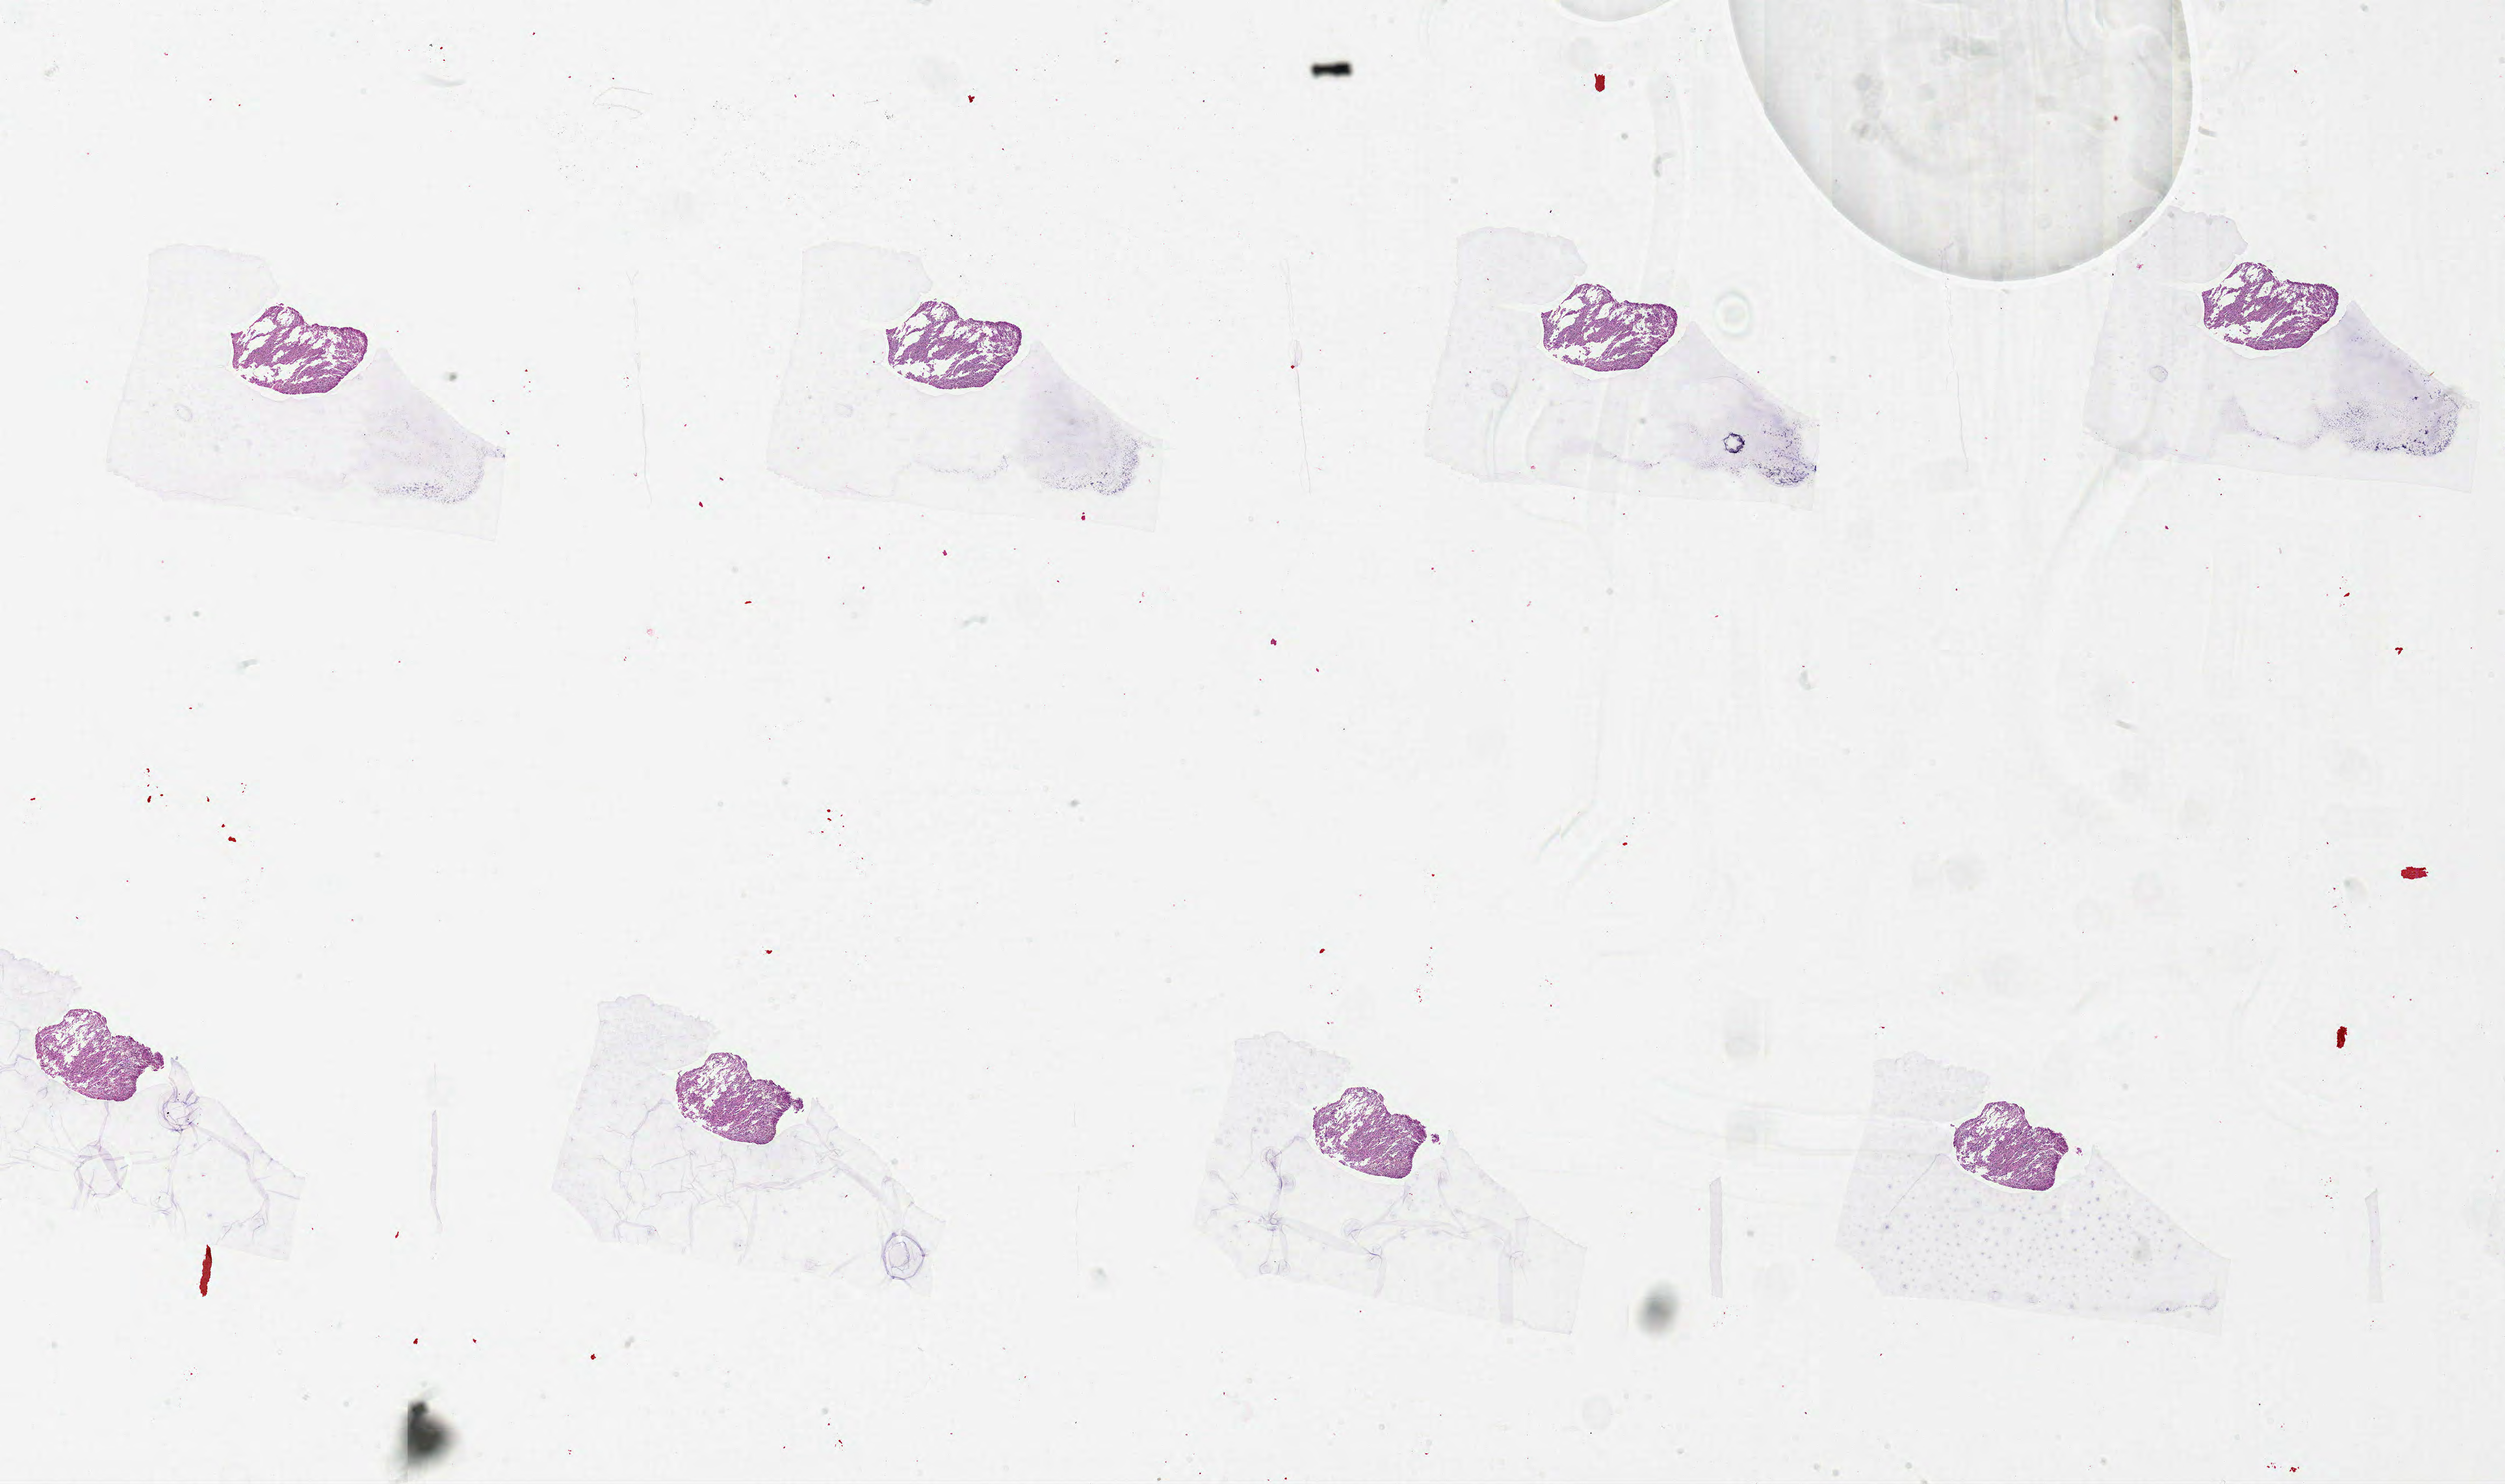
Digitized H&E tissue section (whole slide), a low-resolution overview of the entire scanned area, about 37.0 x 21.9 mm; FFPE section; sample: primary tumour, brain. Patient: male, age at initial diagnosis 52 years.
- histologic diagnosis: Glioblastoma